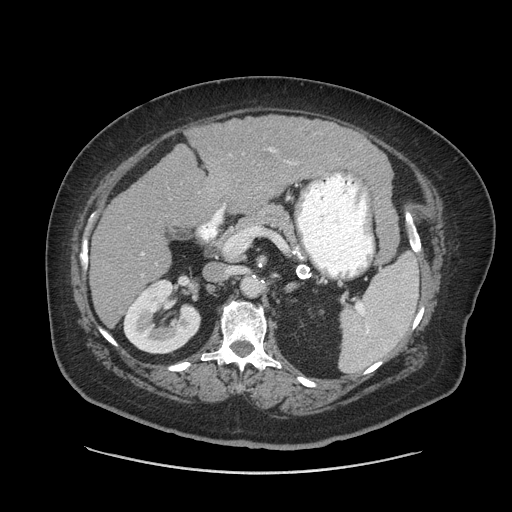
Contrast-enhanced abdominal CT (liver protocol), one axial slice. Reconstruction kernel STANDARD. 140 kVp. Soft-tissue window (W 400 / L 40 HU). 512 × 512 image matrix, field of view 420 × 420 mm. From the clinical record (not read from this slice): diagnosis: hepatocellular carcinoma (patient treated with transarterial chemoembolisation; whether this scan precedes or follows treatment is not stated here); TNM stage (as recorded): Stage-I; Child-Pugh class: A.
Outlined on this slice (semi-automatic segmentation, software-assisted and operator-edited):
- liver parenchyma outside the tumour (the mass and vessels are separate outlines, so this box may not span the whole liver): bounding box [x1, y1, x2, y2] px = [90, 114, 390, 326]
- liver vessels: [141, 148, 290, 255]